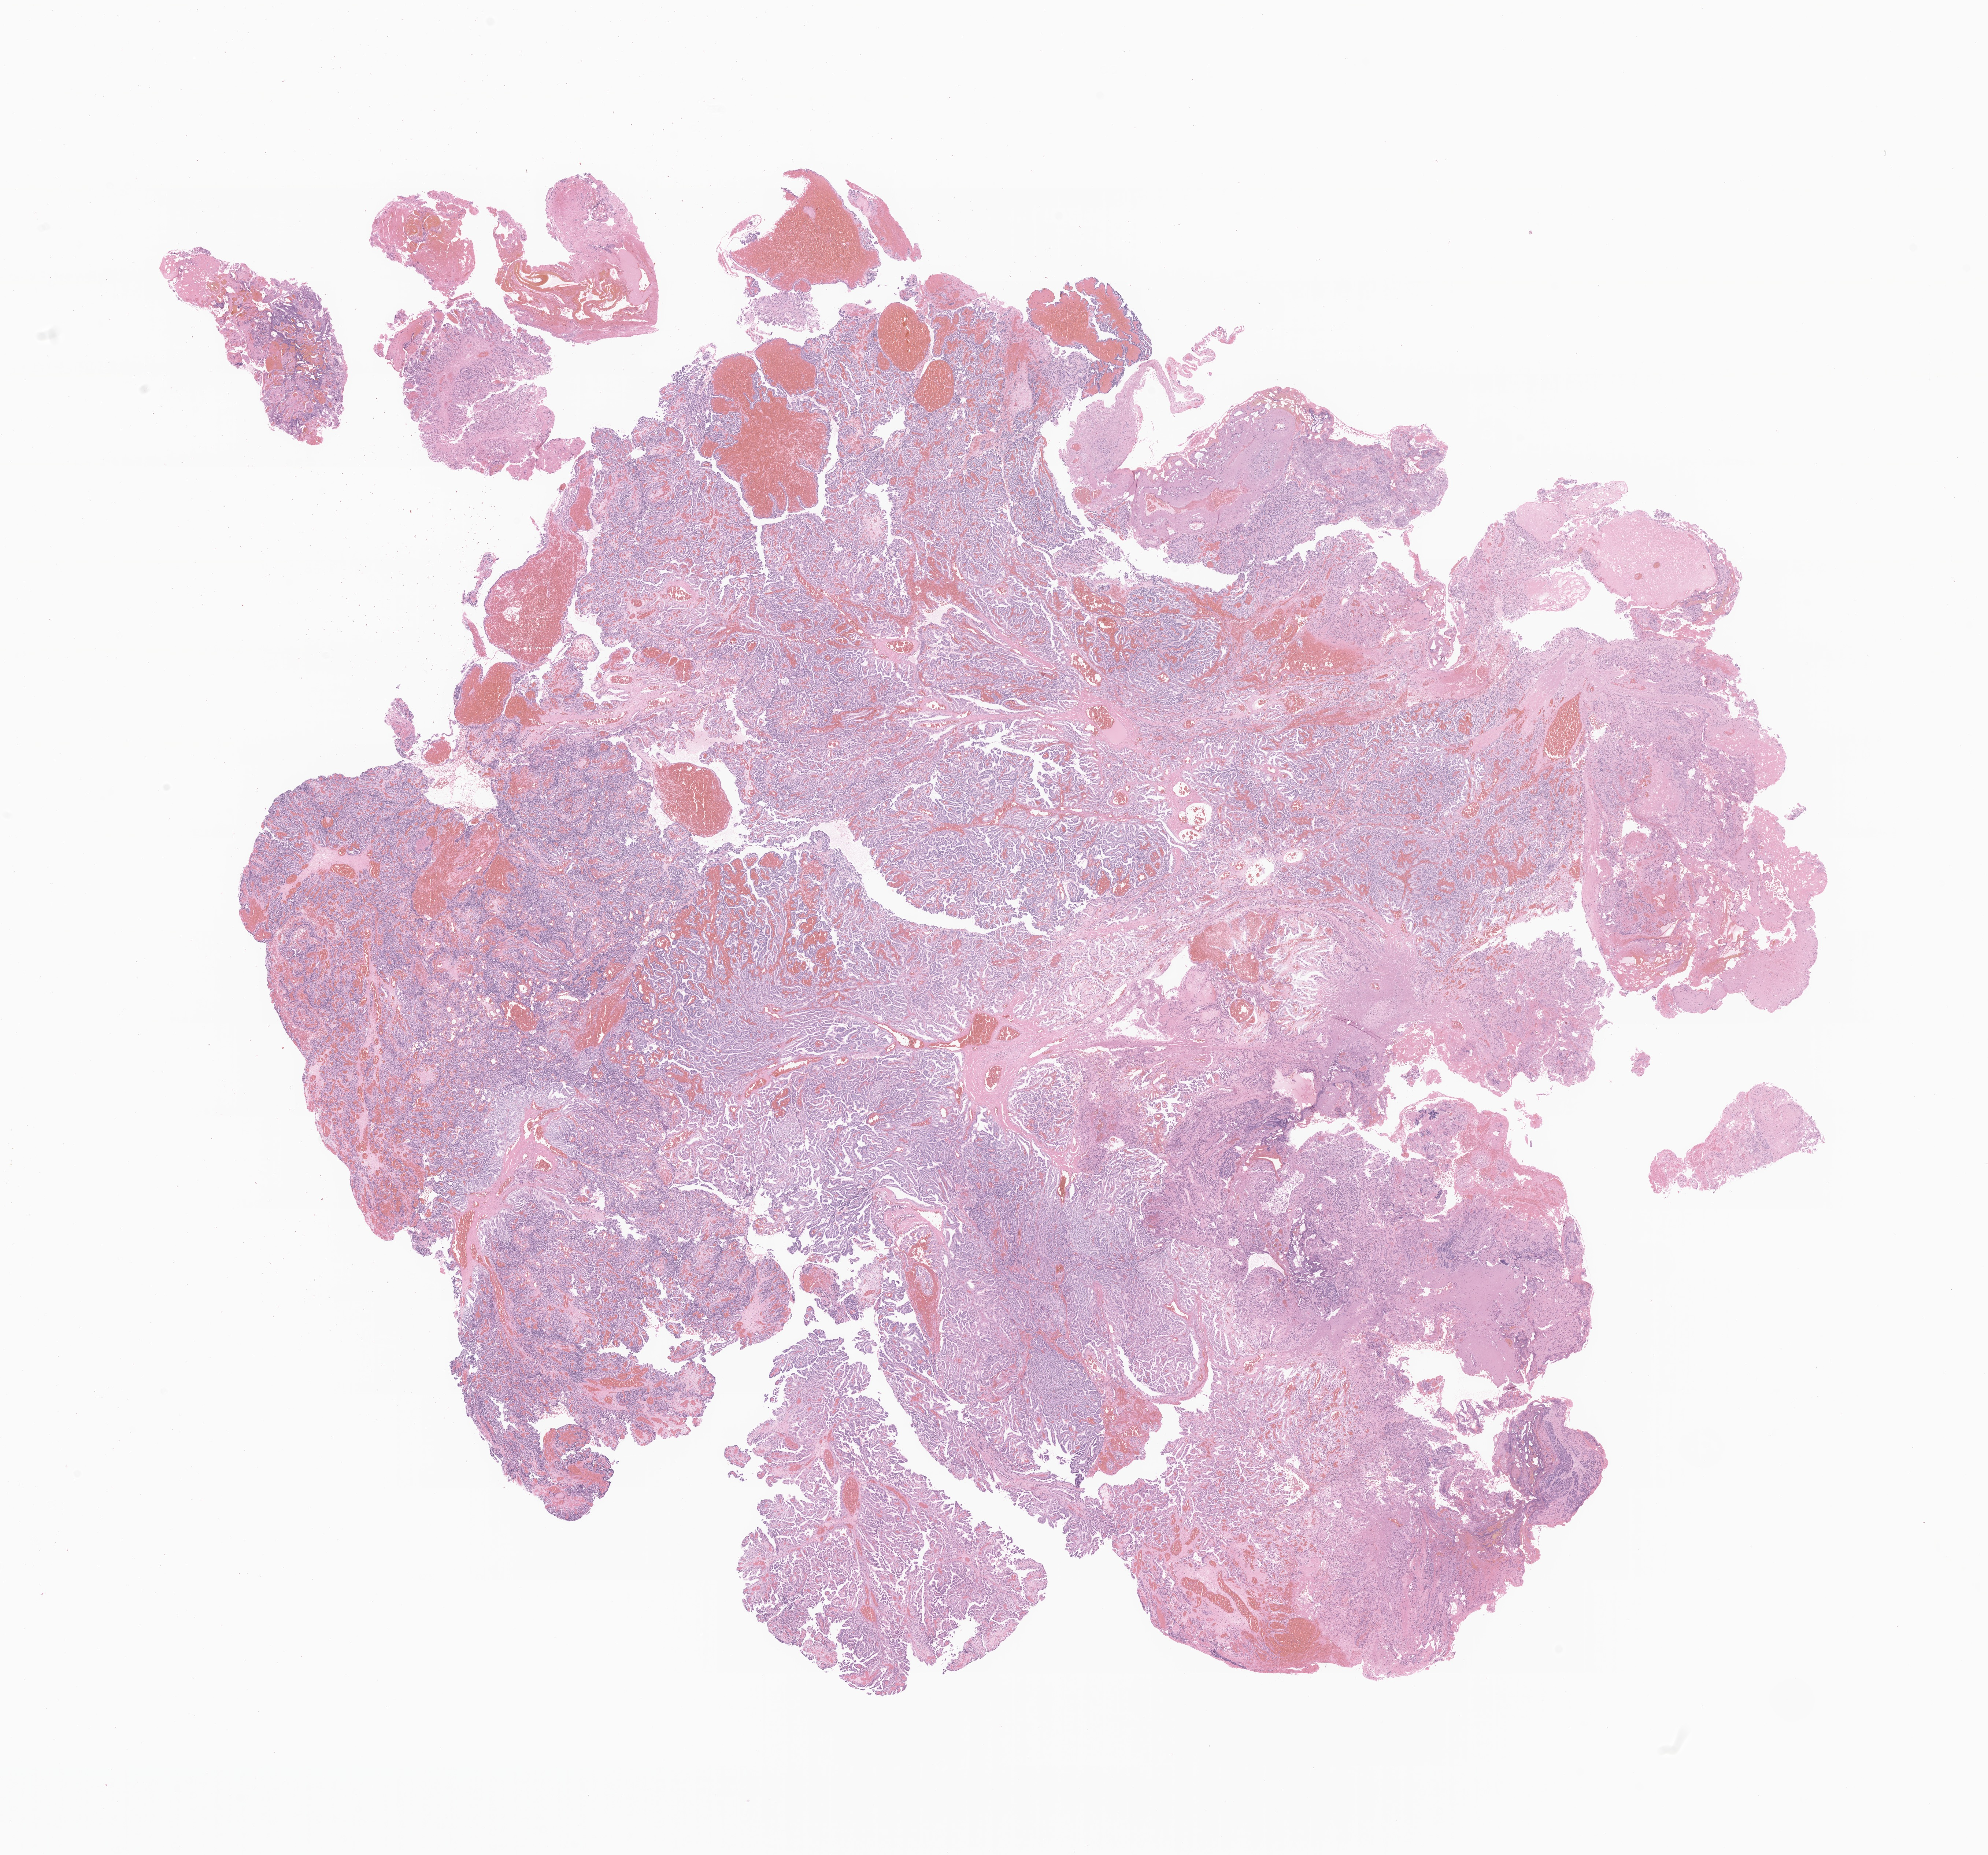
Whole-slide image, H&E stain of tumor tissue from the cerebral ventricle, a low-resolution overview of the entire scanned area, about 22.9 x 21.3 mm; formalin-fixed paraffin-embedded section. Female patient, age 713 days (about 2.0 years).
- diagnosis: Choroid plexus papilloma, NOS